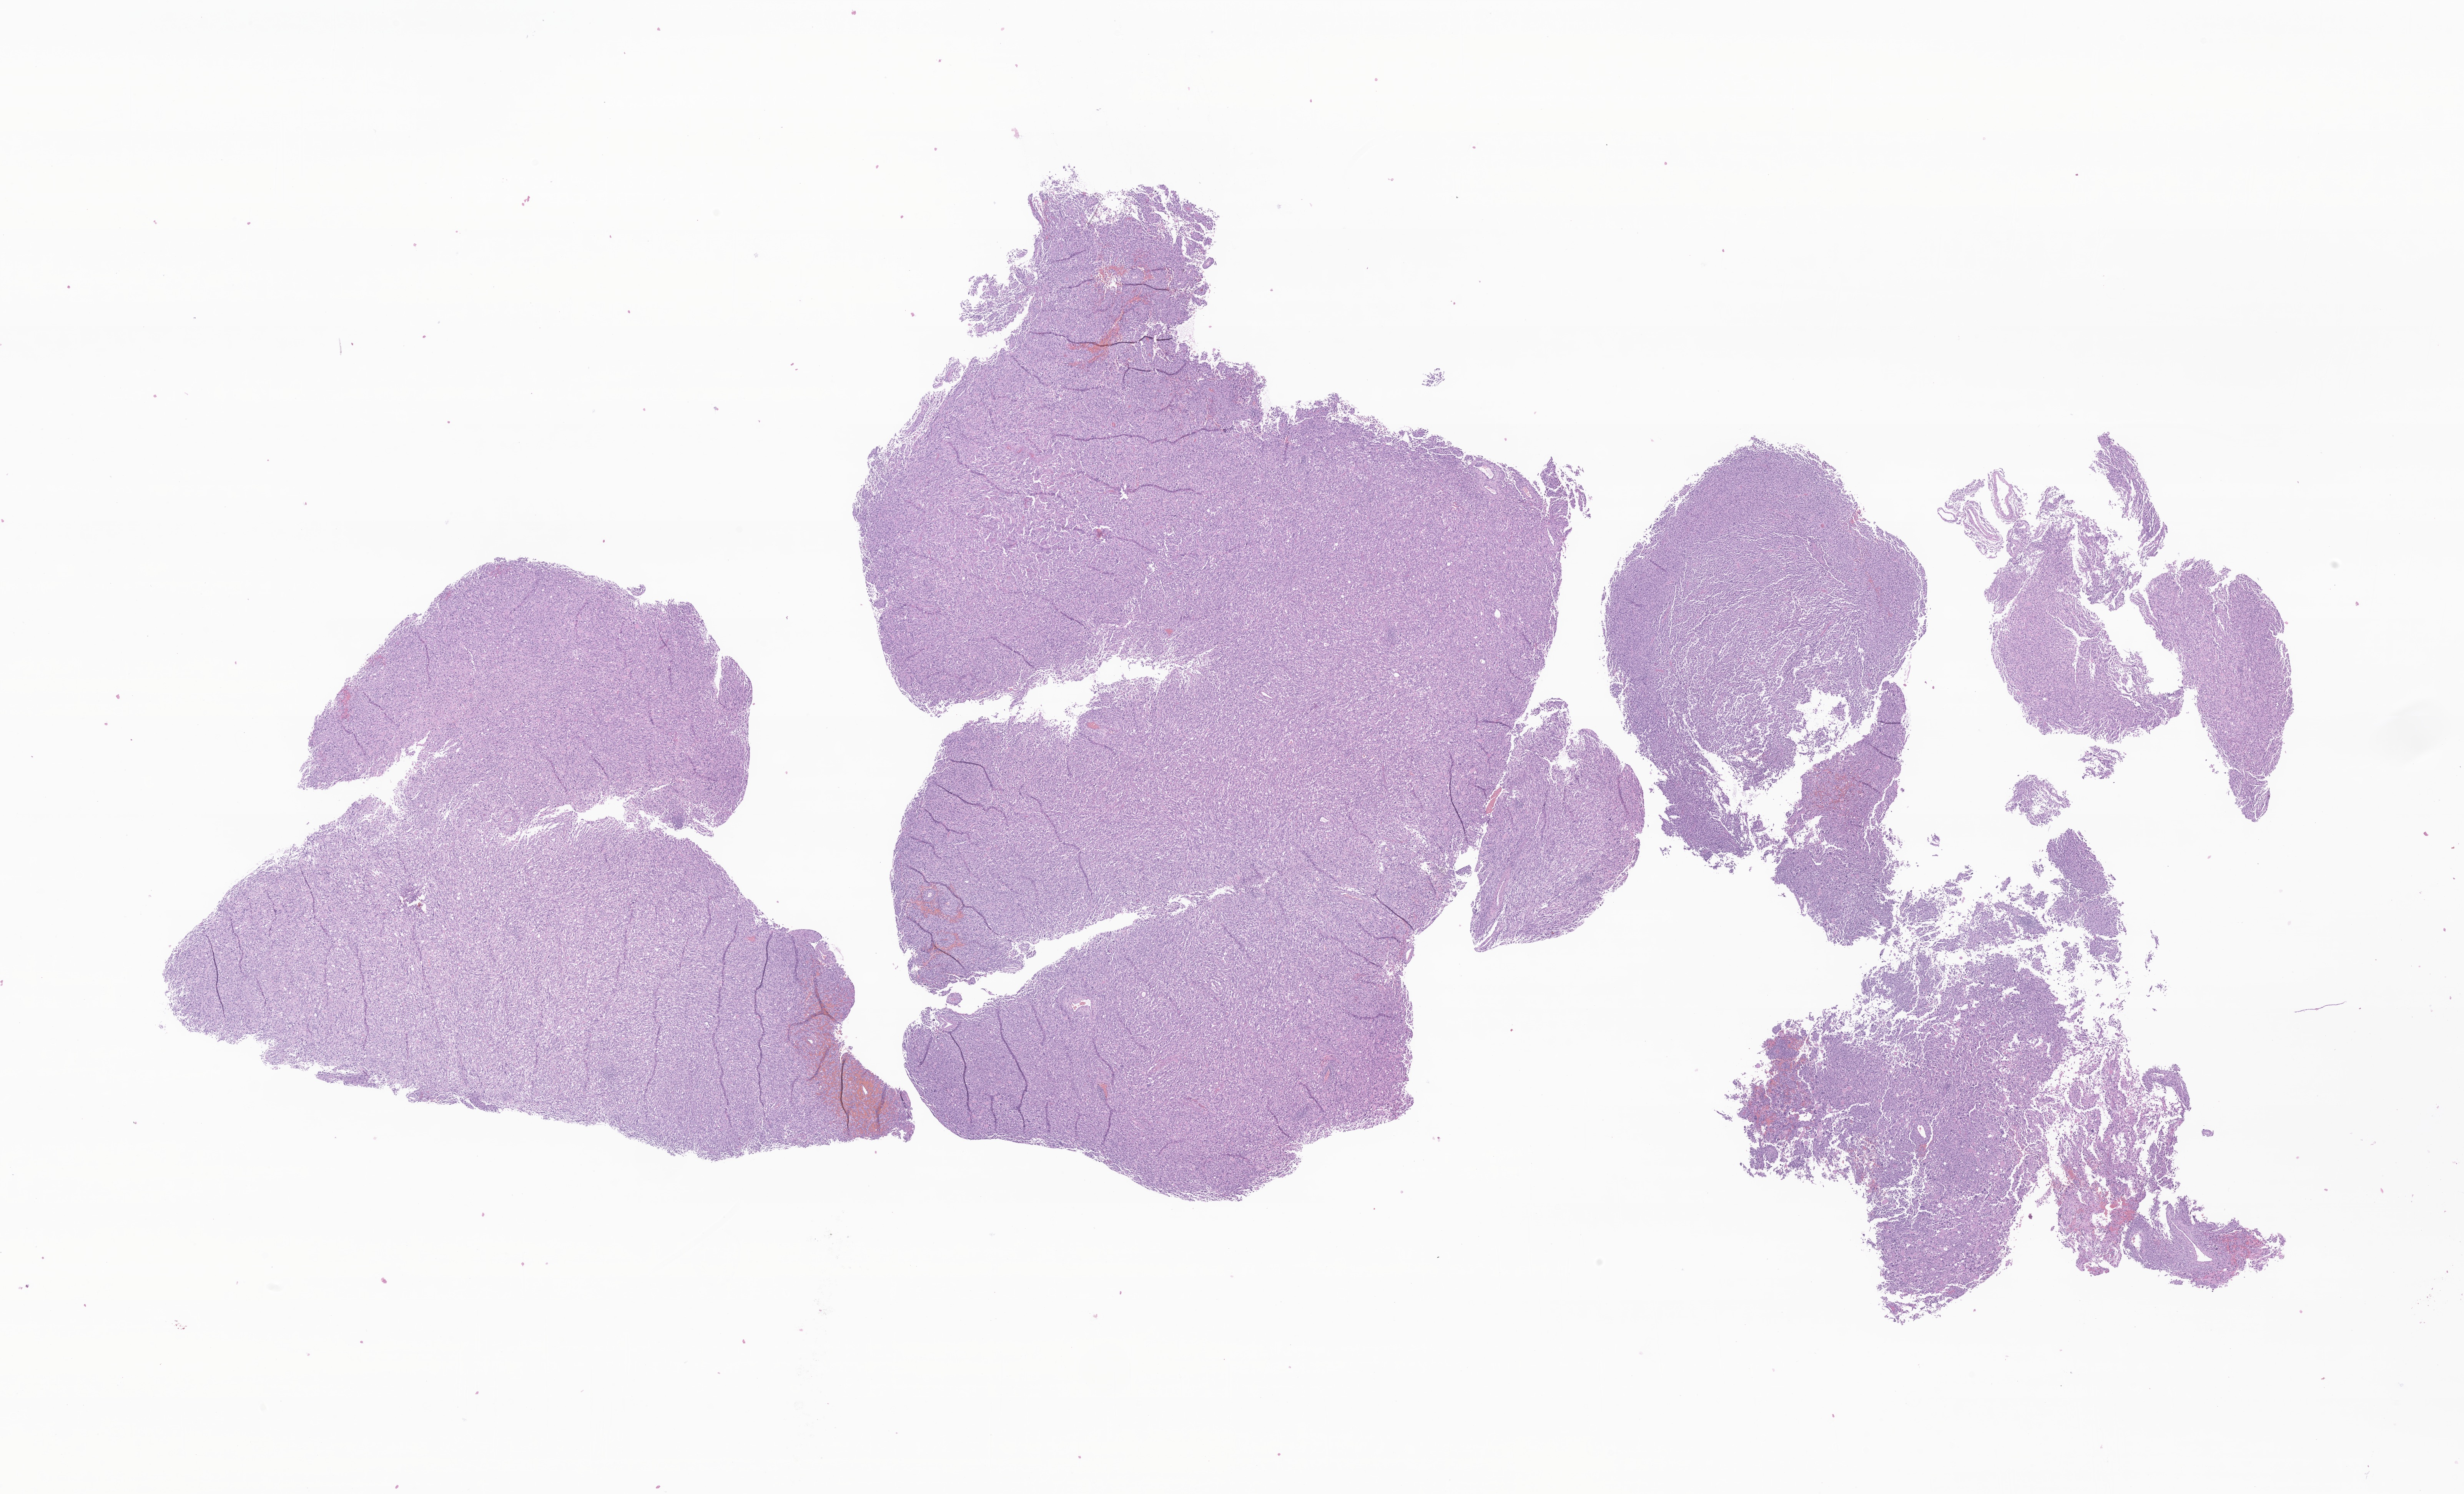
Hematoxylin and eosin (H&E) whole-slide image of tumor tissue from the temporal lobe, whole scanned area (about 27.0 x 16.4 mm) shown as a low-resolution overview. FFPE section. Patient: female, age 130 months (10 years 10 months).
• diagnosis (ICD-O-3 morphology term): Pleomorphic xanthoastrocytoma, NOS